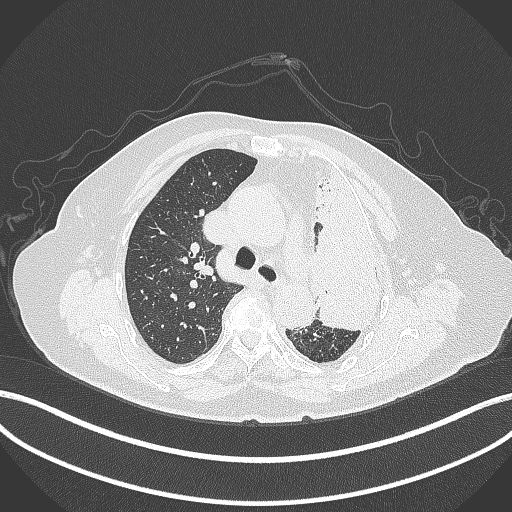
Chest CT, one axial slice. Position 275 of 399 along the scan axis. Lung window (W 1500 / L -600 HU). 1 mm slice thickness. 512 × 512 image matrix, field of view 400 × 400 mm. Patient: female, 75 years. Case-level facts recorded for this patient, not image findings: clinical TNM (as recorded): T3 N3 M1.
Structures marked on this image (rectangle marked by the reading radiologist):
- lung tumour (recorded histology: adenocarcinoma): bounding box [x1, y1, x2, y2] px = [302, 156, 397, 341]